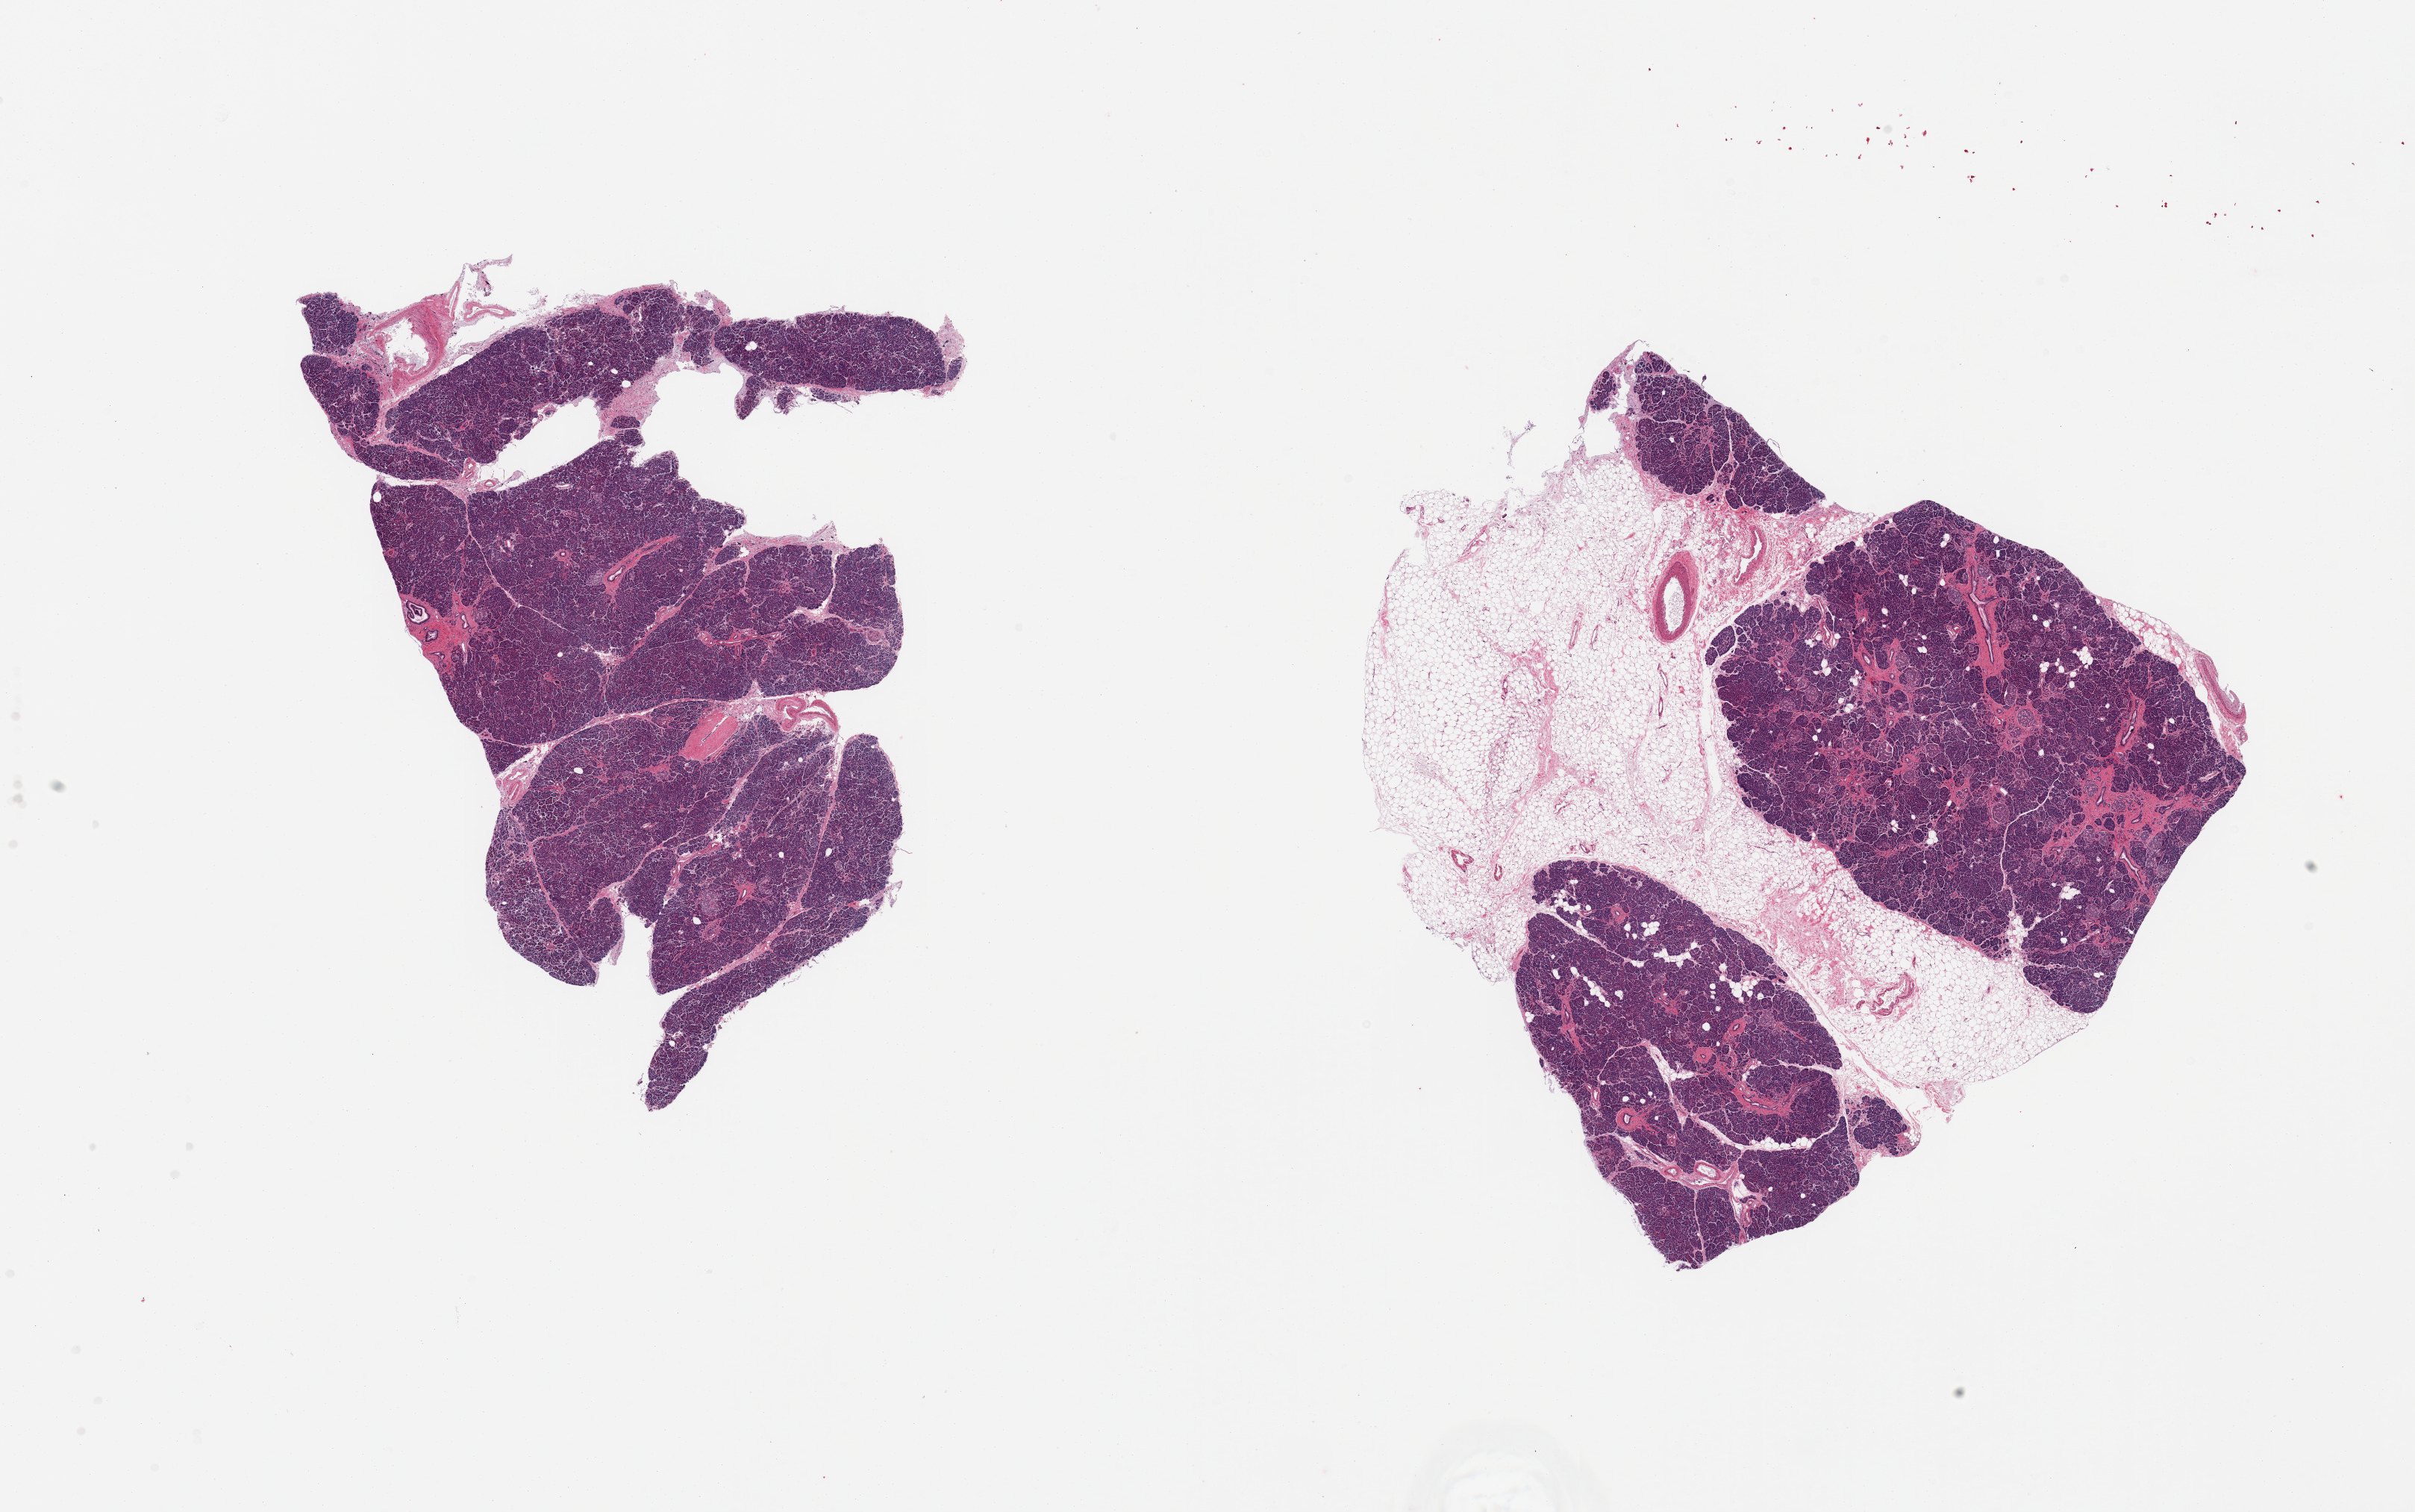
H&E whole-slide image — low-resolution overview of the scanned area, about 25.6 x 16.0 mm (acquisition: 20x scan); PAXgene-fixed paraffin-embedded (PFPE) section; section of pancreas (target tissue); tissue donor sample.
• review note (as recorded): 2 pieces; one piece is ~40% fat (predominantly attached), fibrosis with a relative increase in islets